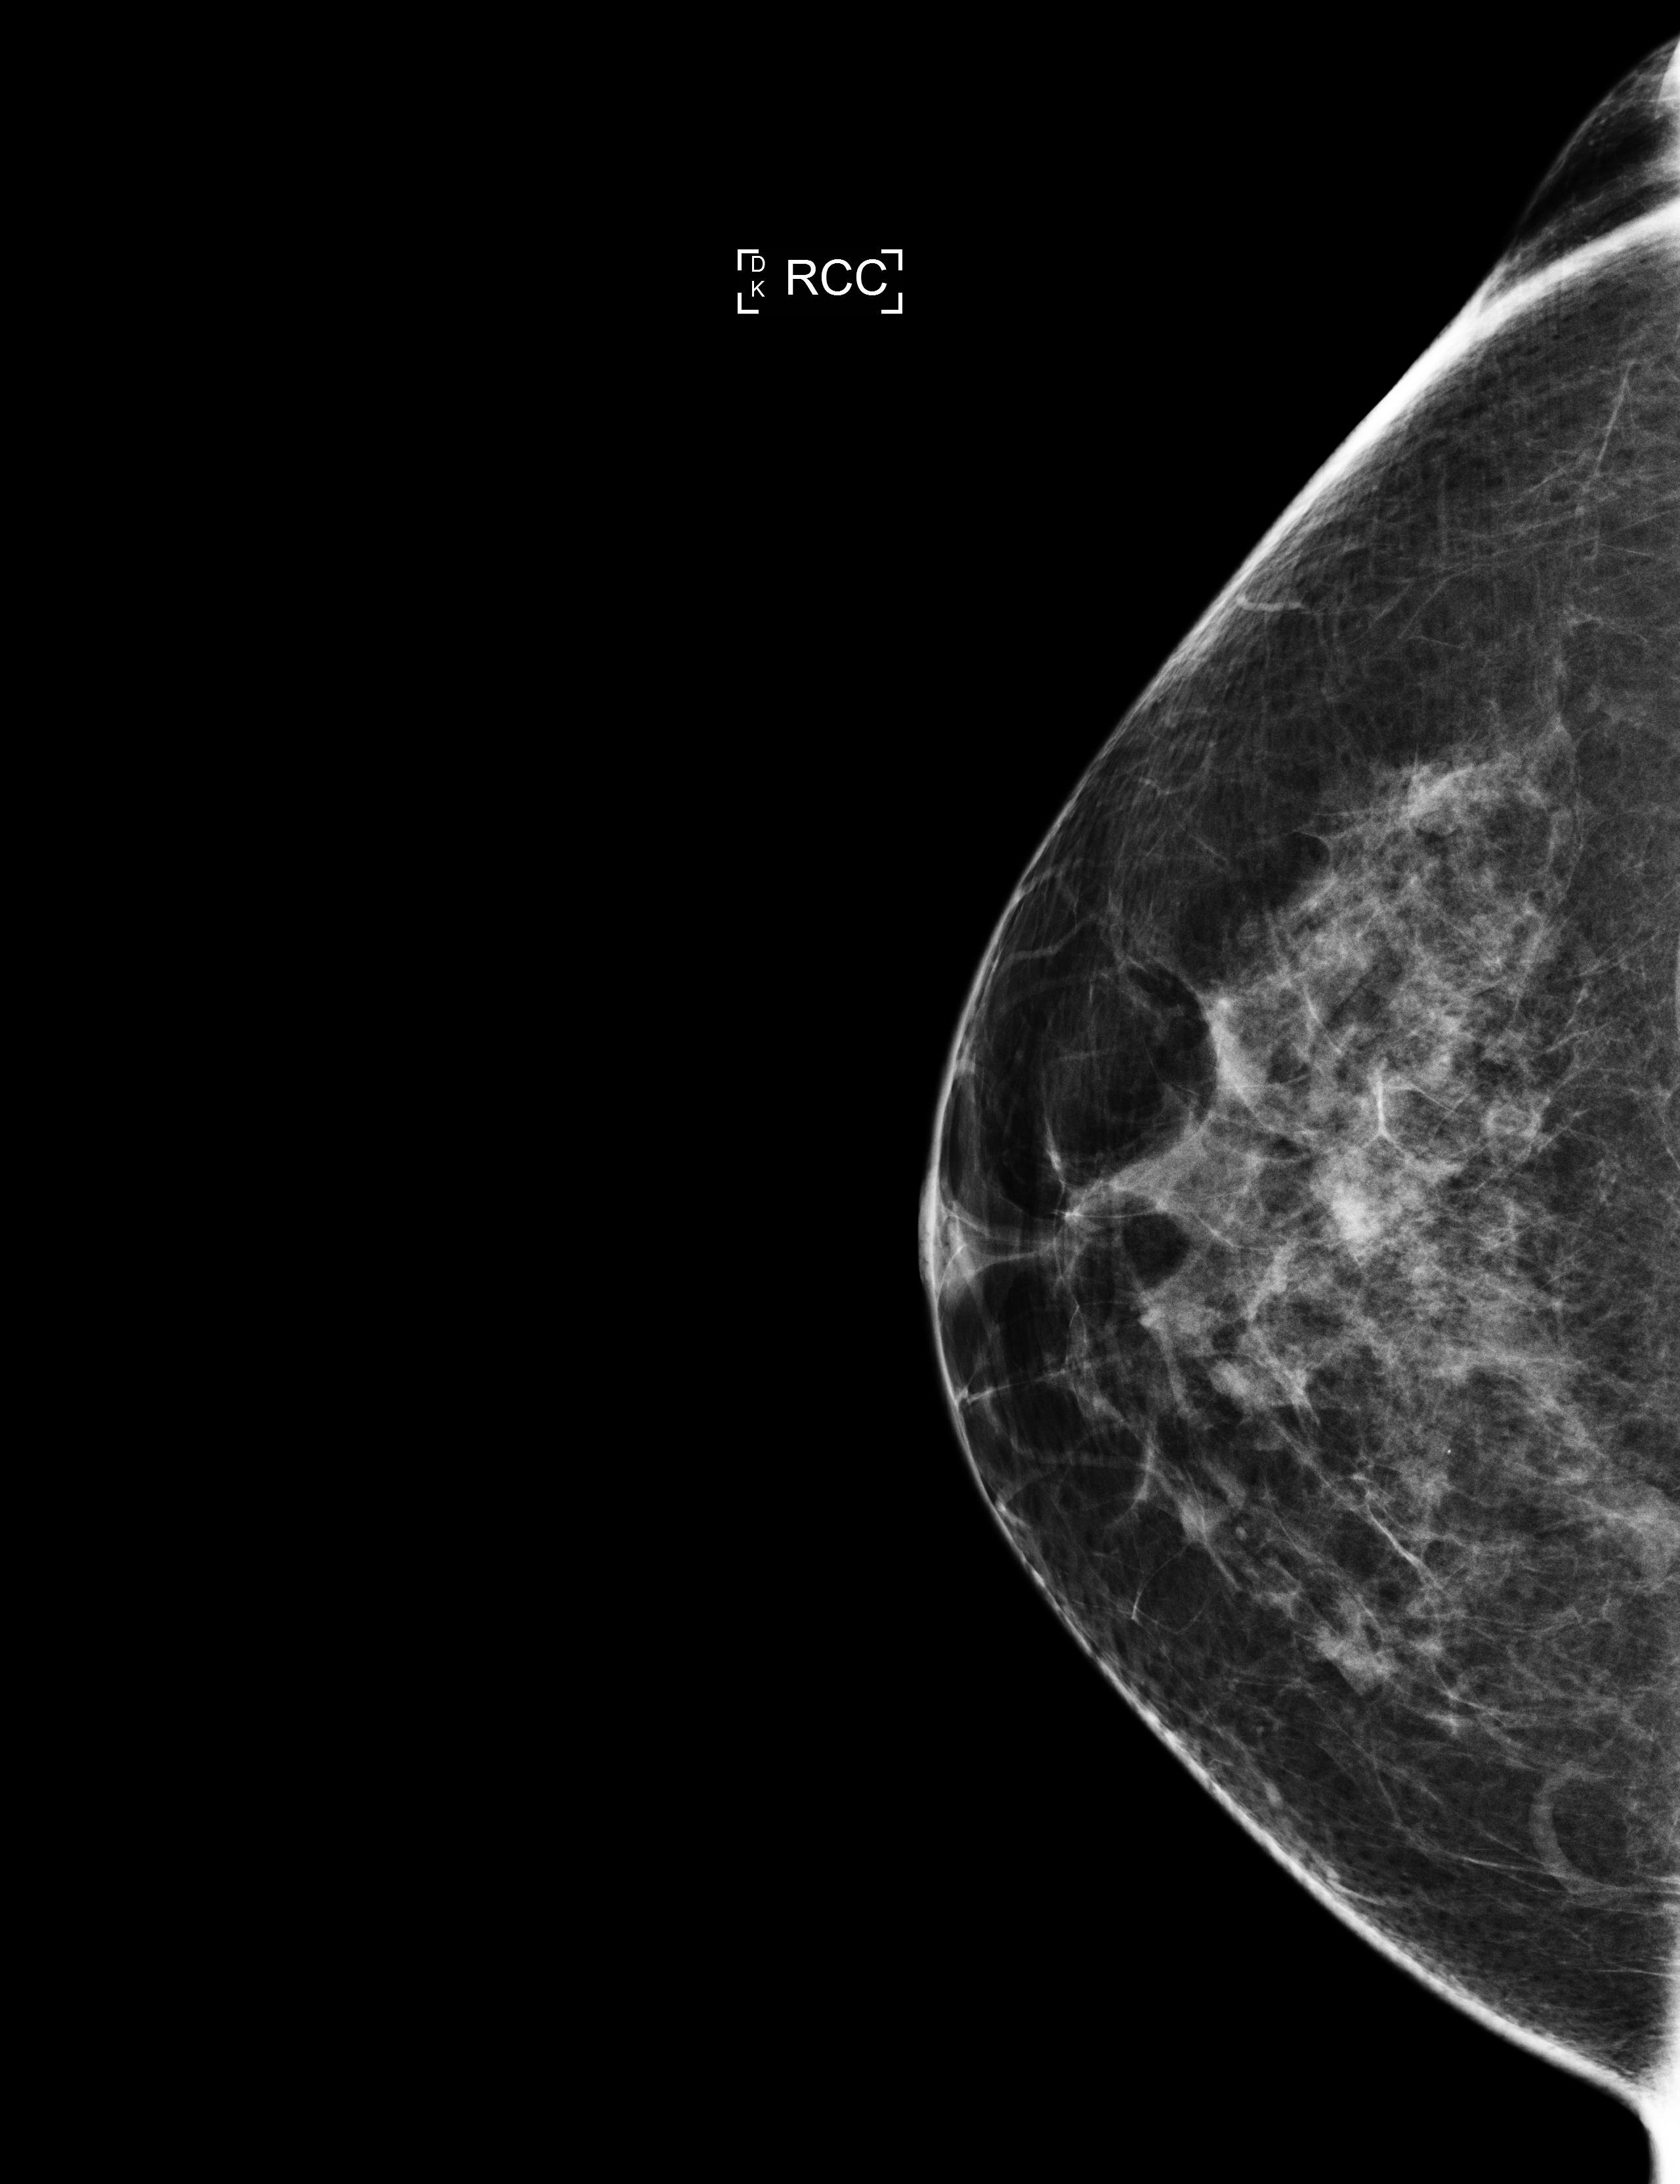
Annual screening mammography examination, compressed breast thickness 65 mm. Patient aged 46 years (female).
Image type: full-field digital mammogram. Breast: right. Projection: craniocaudal (CC) view.